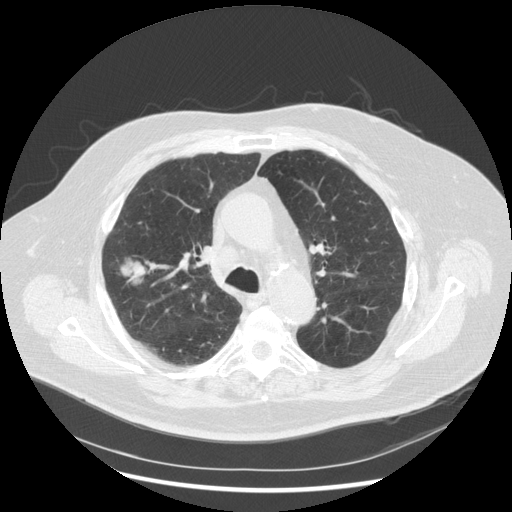
Axial slice from a low-dose chest CT screening exam; third screening round (two years after baseline); lung window (W 1500 / L -600 HU); standard (soft-tissue) reconstruction kernel (STANDARD); 120 kVp; slice 189 of 263 in the series. Male, age 72 years at enrolment. Former smoker at enrolment.
Expert-annotated lung lesion, box from (x=100, y=250) to (x=156, y=298) px. Reader record for this screening exam (exam-level; its link to the box is not recorded): non-calcified nodule or mass ≥4 mm, right upper lobe, 31 × 31 mm, poorly defined margins, soft tissue attenuation, pre-existing on the prior screen: no. Official screen result: positive, other. Lung cancer was diagnosed 70 days after this screen: squamous cell carcinoma, NOS, right upper lobe, poorly differentiated (G3), stage IIIA (AJCC 6th edition), 19 mm at pathology.